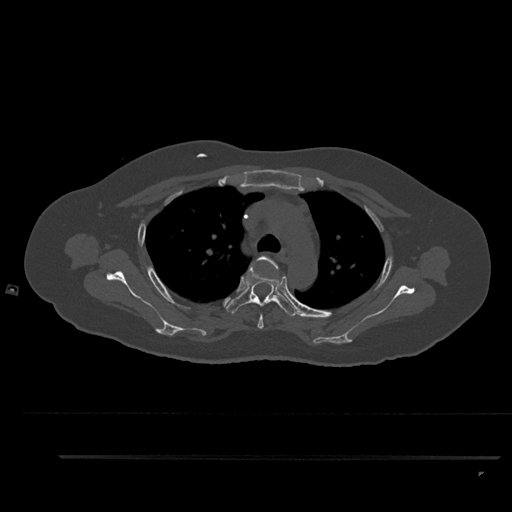
CT including the spine, one axial slice. Position 656 of 797 along the scan axis. Reconstruction kernel Br40s/3. 120 kVp. Bone window (W 1800 / L 400 HU). 0.5 mm slice thickness. 512 × 512 image matrix, field of view 408 × 408 mm. Female patient, age 44 years. From the clinical record (not read from this slice): primary cancer: renal; vertebrae with lytic lesions (as recorded): L1.
Outlined on this slice (semi-automatically segmented with operator editing):
- T3 vertebra: bounding box (x1, y1, x2, y2) in pixels: (251, 256, 279, 329)
- T4 vertebra: (226, 266, 298, 317)